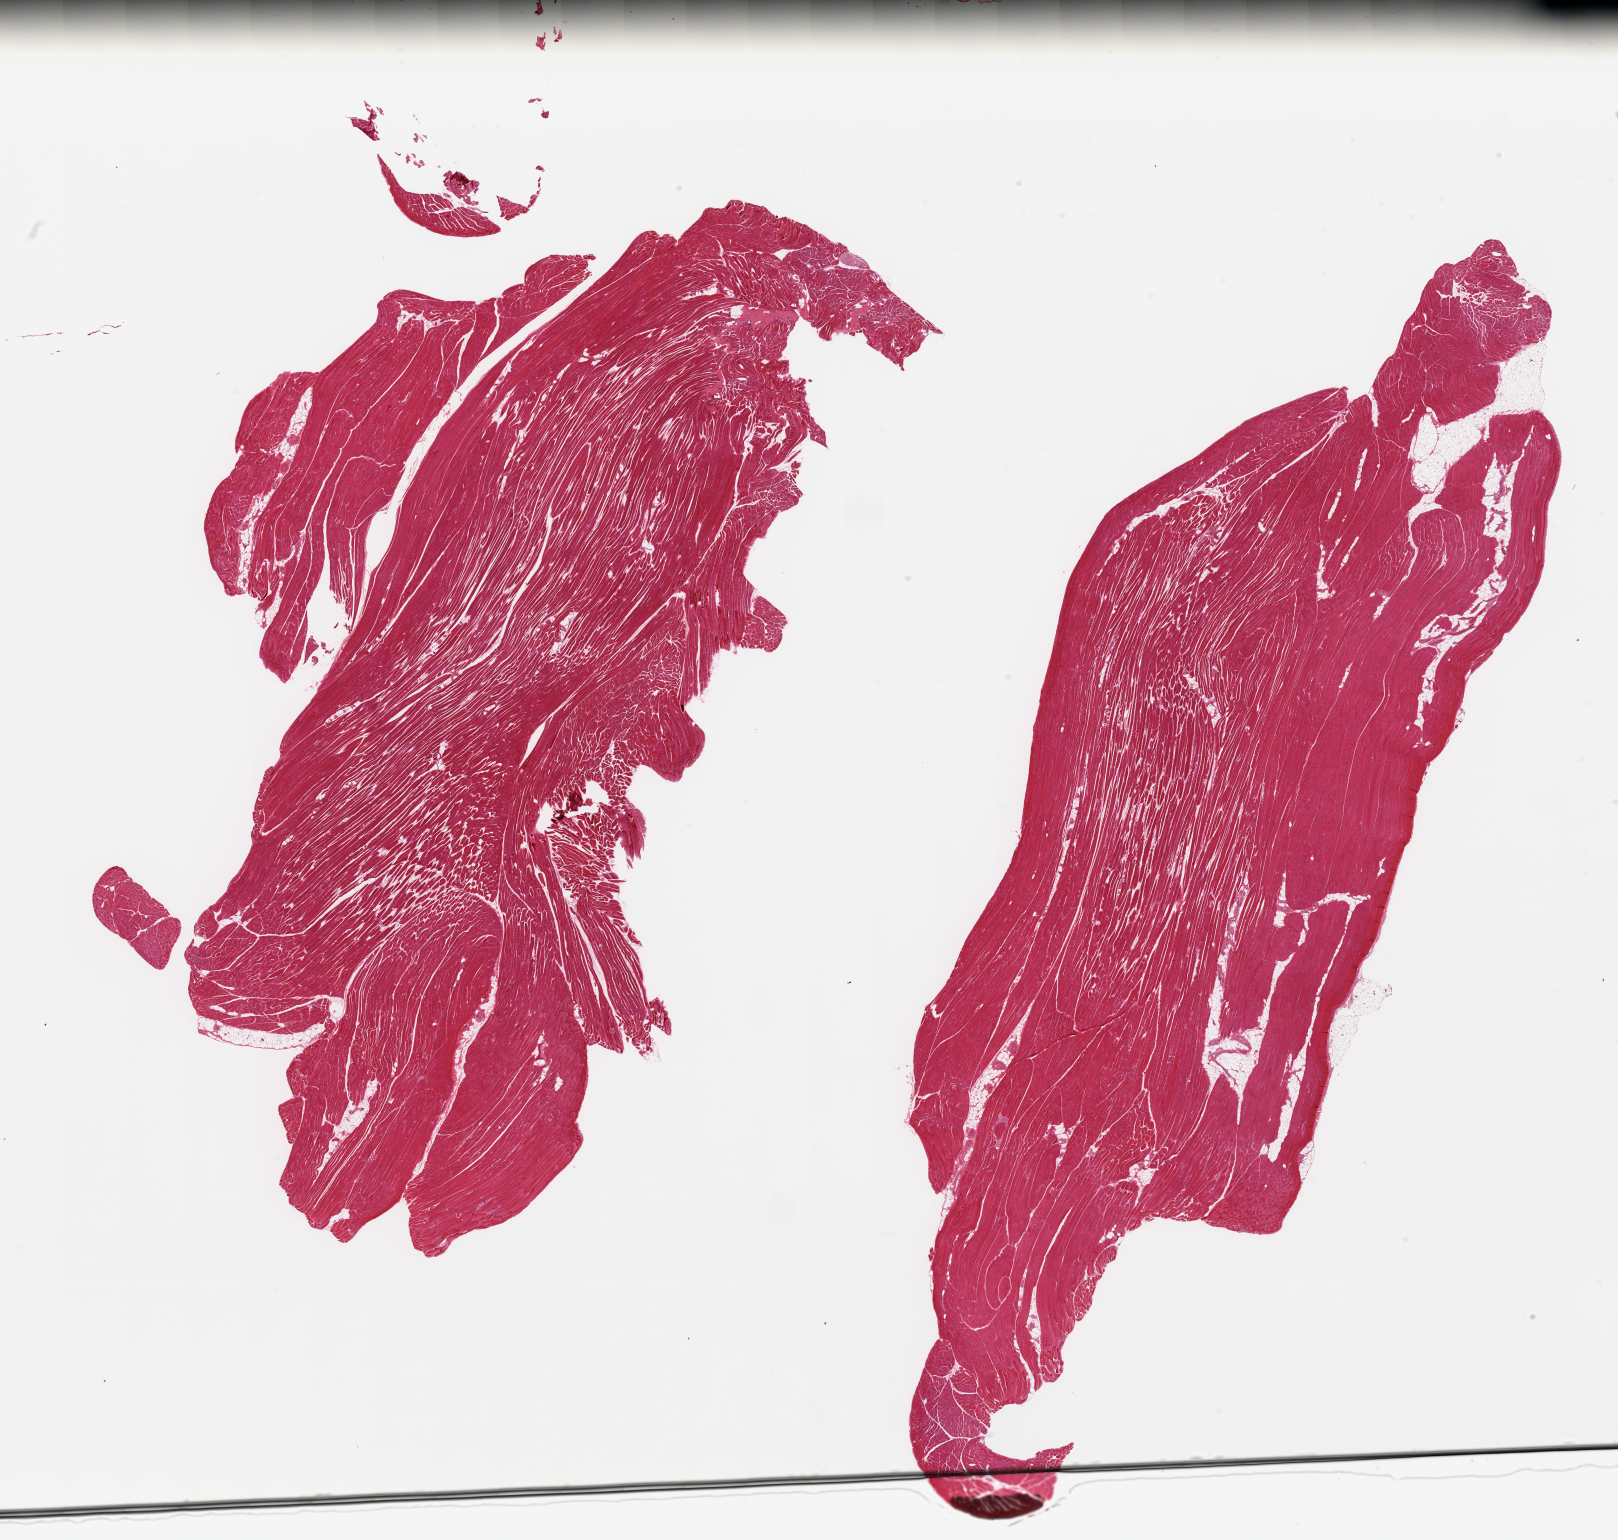
Digitized hematoxylin and eosin (H&E)-stained section, low-resolution overview of the scanned area, about 25.6 x 24.4 mm; PAXgene-fixed, paraffin-embedded tissue; sampled site (target tissue): skeletal muscle; donor tissue sample. Donor: male.
* reviewer comment on this tissue sample: 2 pieces; includes from 5-10% internal fat